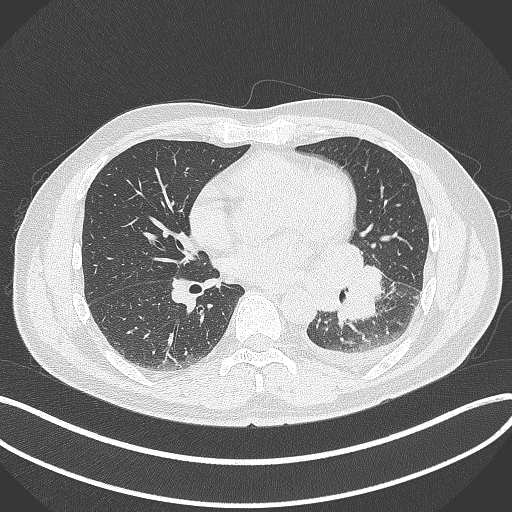
Chest CT, one axial slice. Position 165 of 342 along the scan axis. Reconstruction kernel B70f. 120 kVp. Lung window (W 1500 / L -600 HU). 512 × 512 image matrix. Patient: male, 58 years. Case-level facts recorded for this patient, not image findings: clinical TNM (as recorded): T3 N1 M1b.
Annotated regions visible in this slice (bounding box drawn by a radiologist):
- lung tumour (recorded histology: small cell carcinoma): bounding box (x1, y1, x2, y2) in pixels: (312, 236, 386, 329)